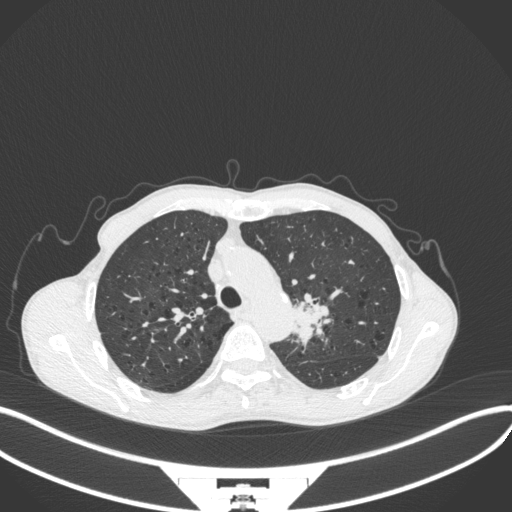
Chest CT, one axial slice; position 309 of 394 along the scan axis; 120 kVp; lung window (W 1500 / L -600 HU); 1 mm slice thickness; 512 × 512 image matrix. Patient: male, 65 years. Case-level facts recorded for this patient, not image findings: clinical TNM (as recorded): T2b N0 M0.
Structures marked on this image (bounding box drawn by a radiologist):
- lung tumour (recorded histology: adenocarcinoma): bounding box <290,294,334,353> (left, top, right, bottom; pixels)